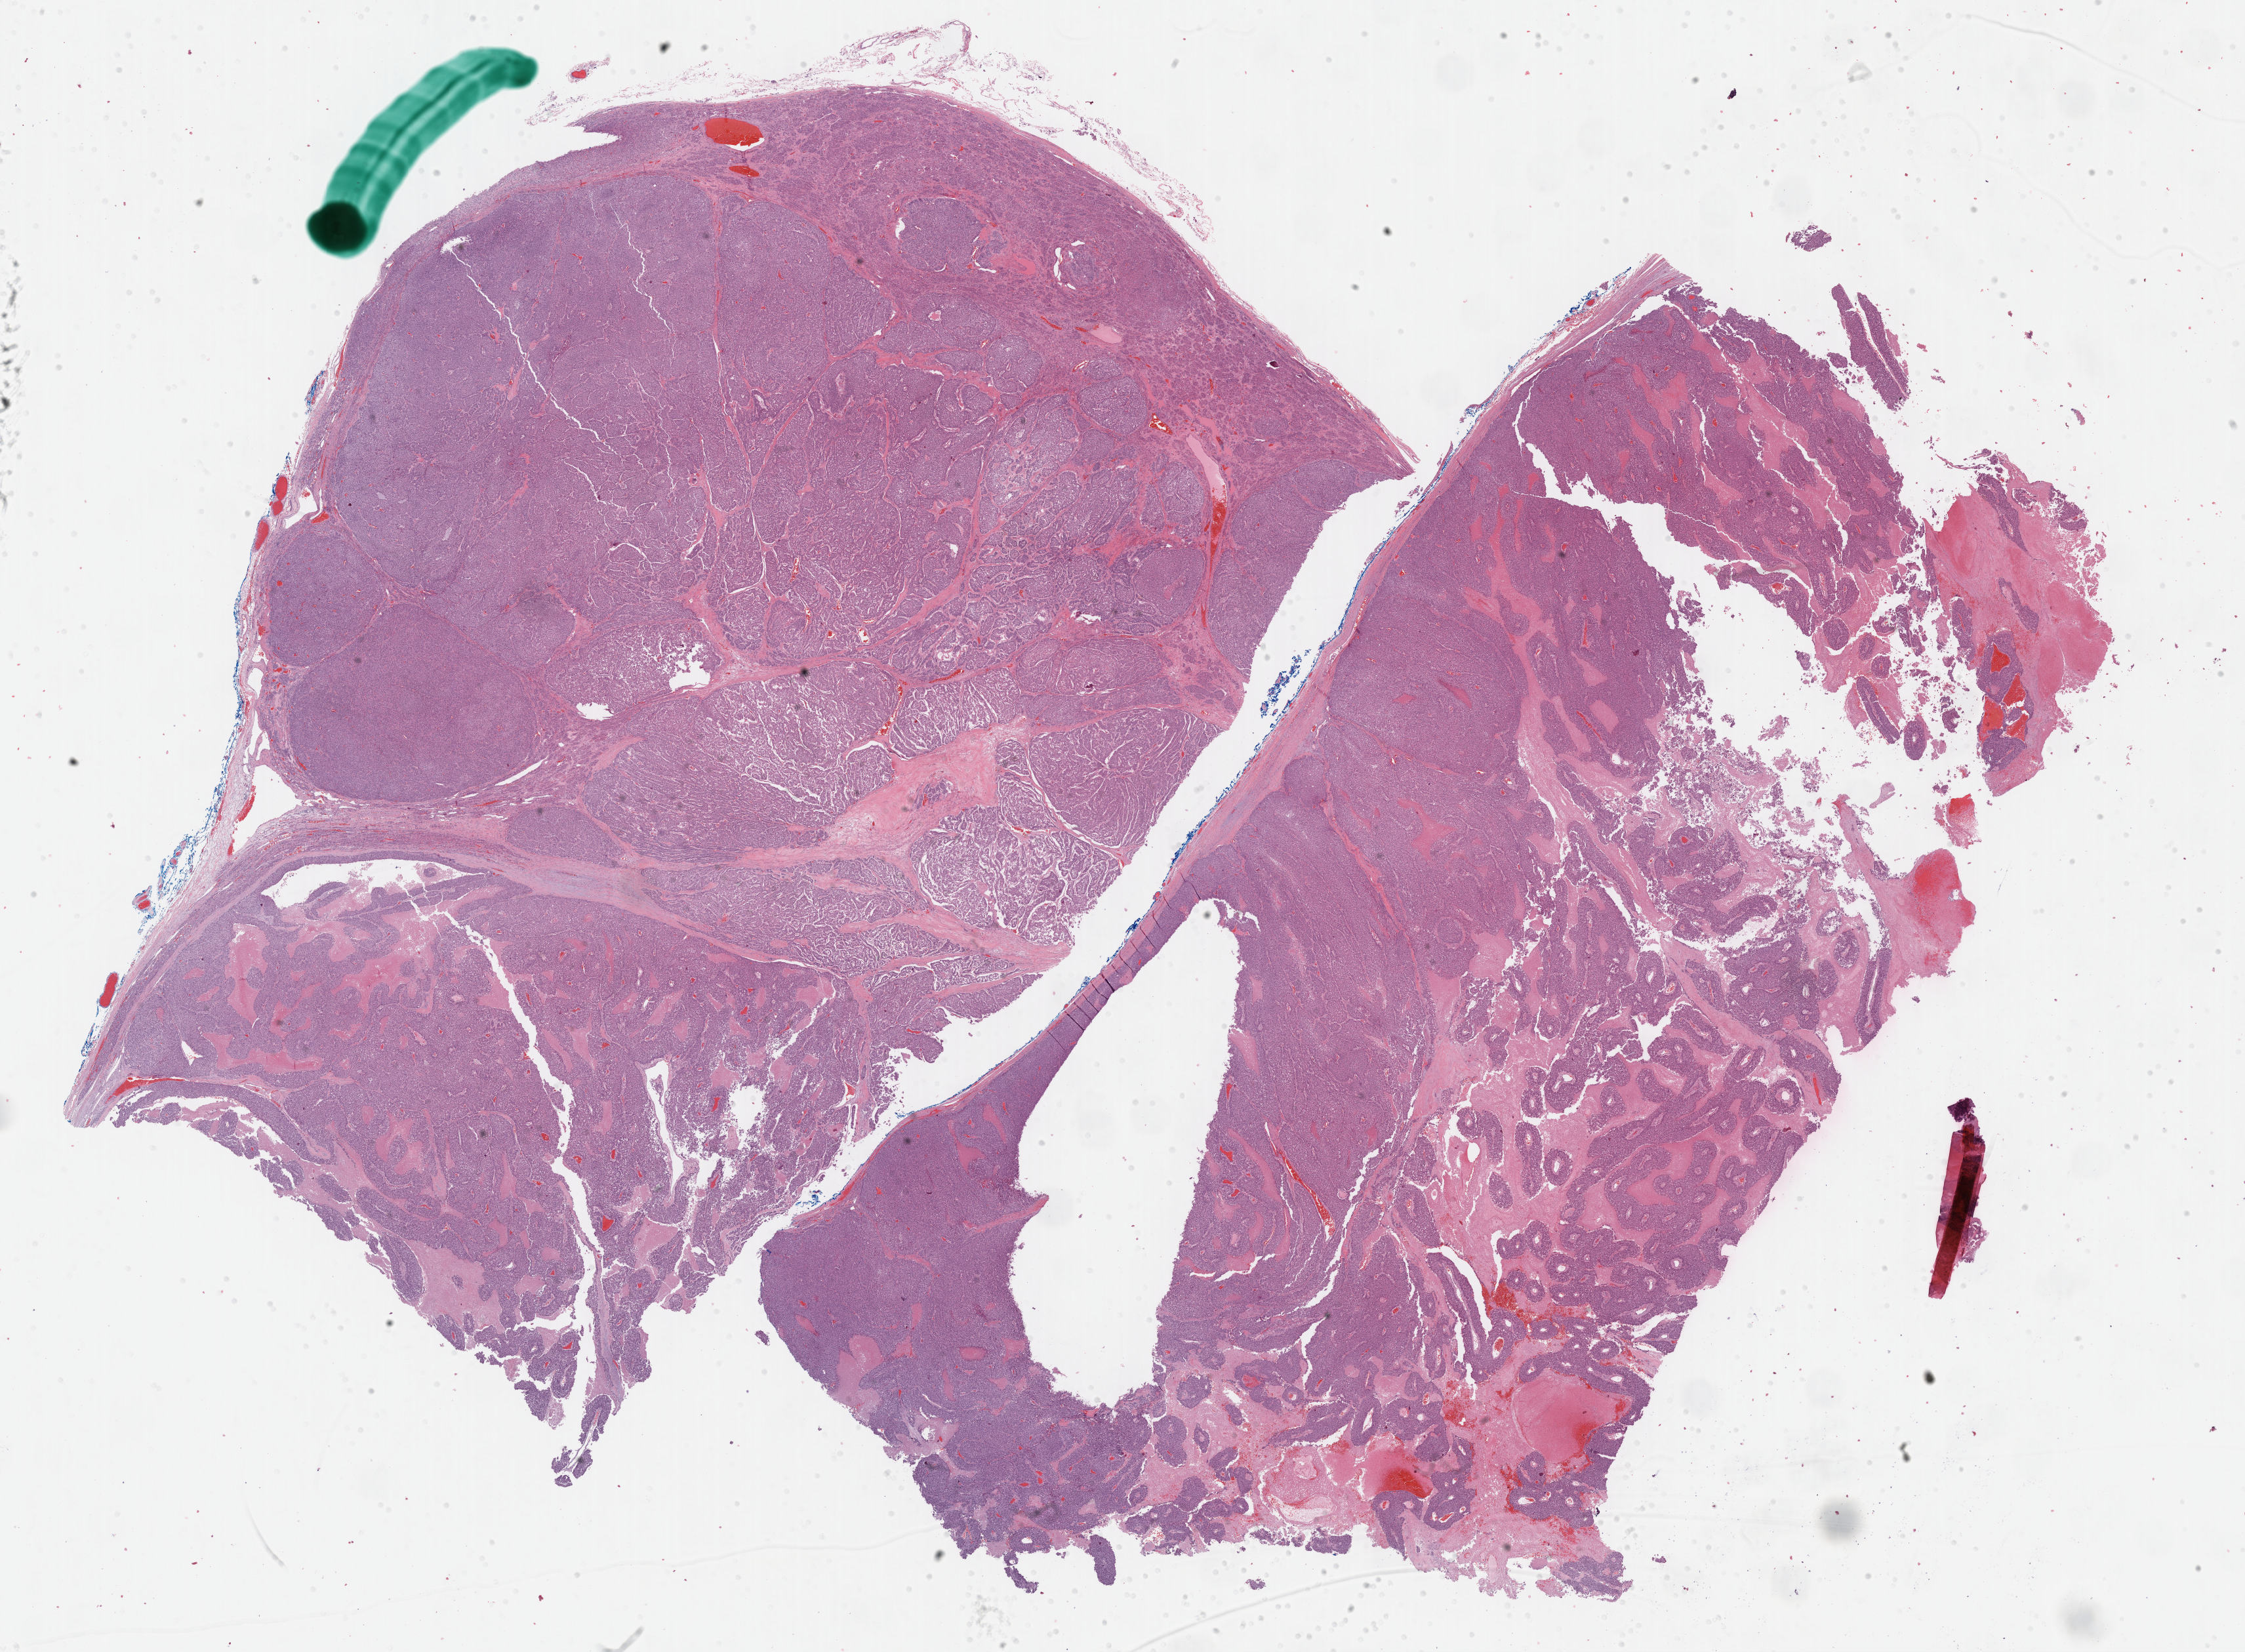
Digitized H&E-stained tissue section (whole slide) — a low-resolution overview of the entire scanned area, about 27.7 x 20.4 mm (slide scanned at 40x); FFPE section; sample: primary tumour, adrenal cortex. Female, age 69 years at initial diagnosis.
Diagnosis: Adrenal cortical carcinoma.